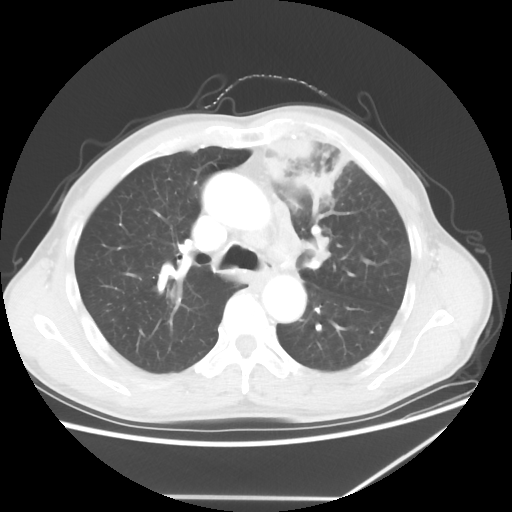
Chest CT, one axial slice; slice 42 of 64 in the series (ordered by position); reconstruction kernel STANDARD; 100 kVp; lung window (W 1500 / L -600 HU); 5 mm slice thickness; 512 × 512 image matrix, field of view 383 × 383 mm. Male patient, age 64 years. Case-level facts recorded for this patient, not image findings: clinical TNM (as recorded): T1c N1 M1; histopathological grade: G2.
Structures marked on this image (bounding box drawn by a radiologist):
- lung tumour (recorded histology: squamous cell carcinoma): bounding box (x1, y1, x2, y2) in pixels: (258, 130, 344, 216)